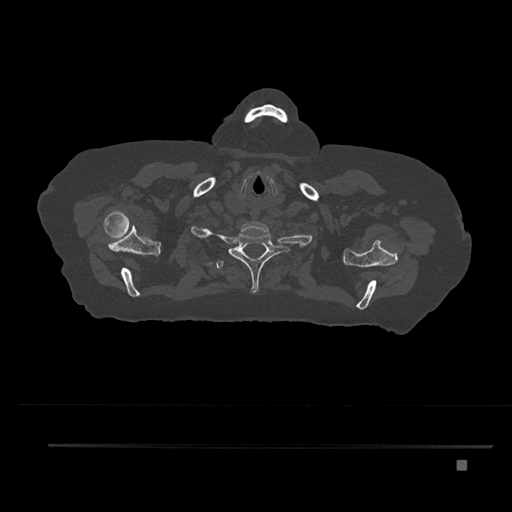
CT including the spine, one axial slice; position 698 of 797 along the scan axis; bone window (W 1800 / L 400 HU); 0.5 mm slice thickness; 512 × 512 image matrix, field of view 437 × 437 mm. Female patient, age 76 years. From the clinical record (not read from this slice): primary cancer: lung; vertebrae with lytic lesions (as recorded): T11, L3.
Annotated regions visible in this slice (semi-automatic segmentation, software-assisted and operator-edited):
- T1 vertebra: bounding box [x1, y1, x2, y2] px = [228, 232, 283, 293]
- T2 vertebra: [216, 247, 235, 269]